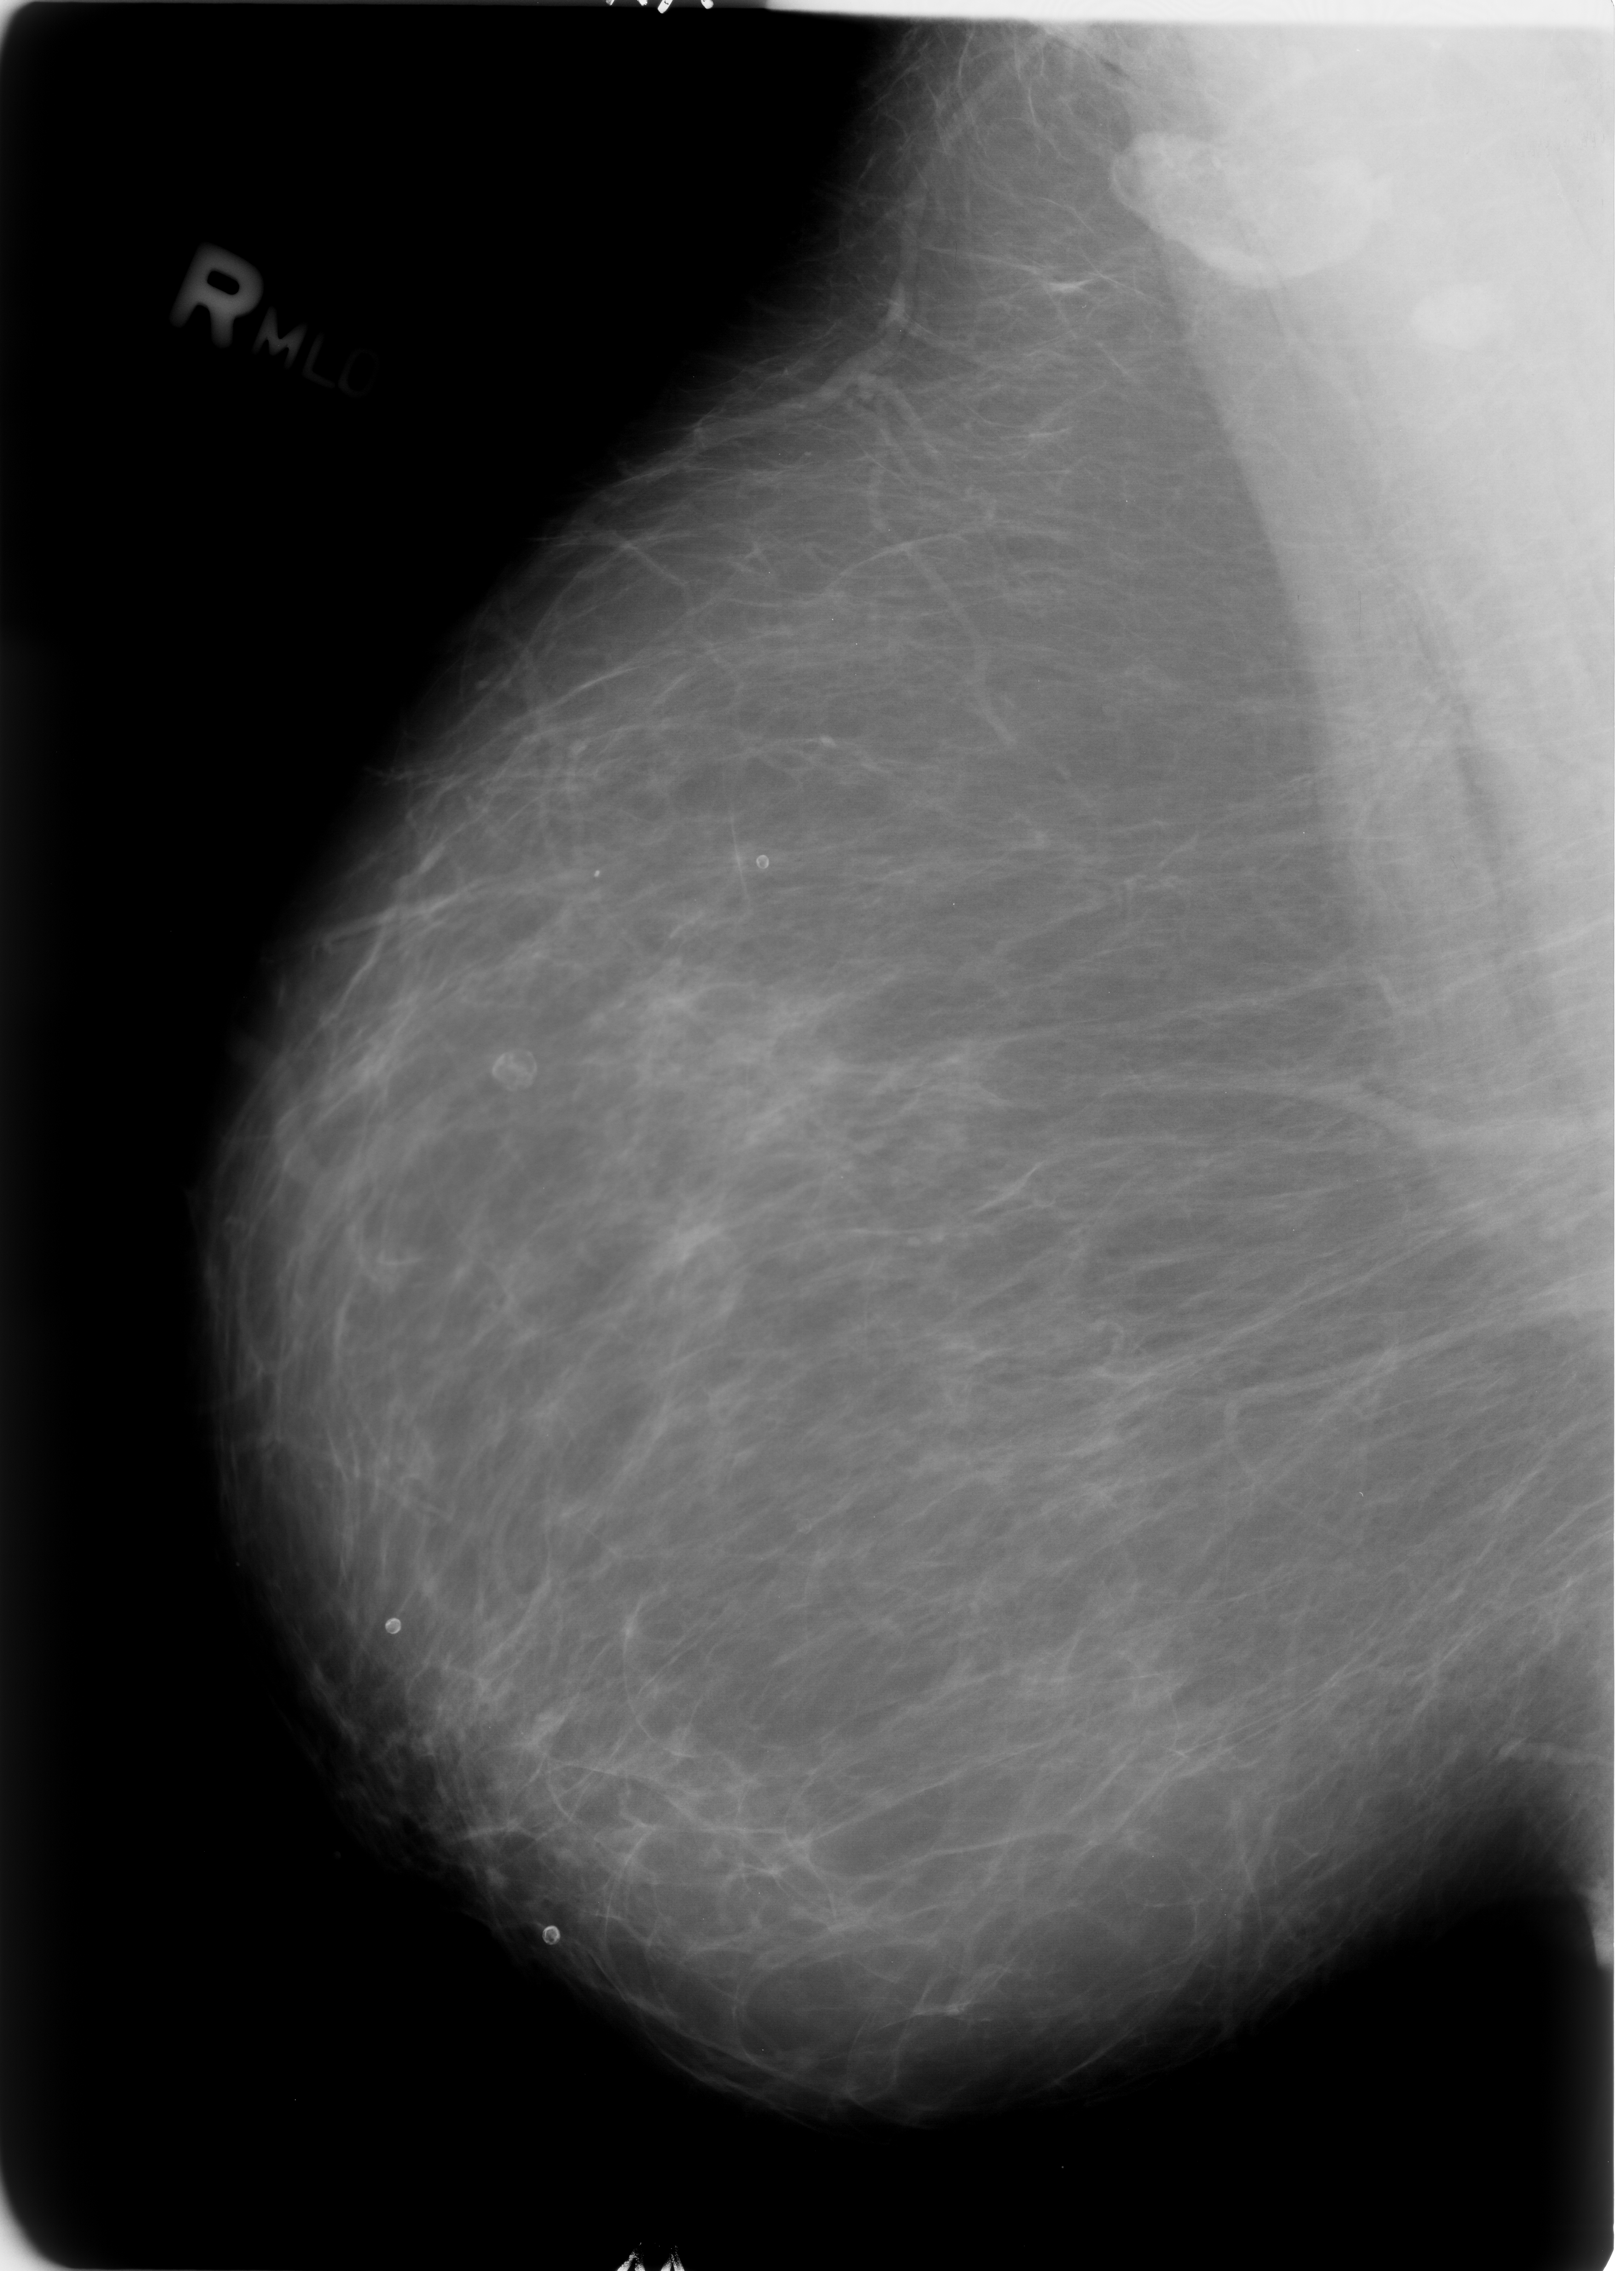
Scanned film-screen mammogram. Right breast. Mediolateral oblique (MLO) view. Breast composition: almost entirely fatty (BI-RADS density category 1 of 4). 1624 × 2271 image matrix.
Expert-marked regions of interest on this film, with their recorded descriptors:
- Finding 1 of 2: calcifications, morphology eggshell; BI-RADS assessment category 2; subtlety rating 5 on a 1 (subtle) to 5 (obvious) scale; benign; no additional work-up was recommended (outcome (as recorded, no biopsy): benign without callback): bounding box <479,1047,543,1095> (left, top, right, bottom; pixels)
- Finding 2 of 2: calcifications, morphology eggshell; BI-RADS assessment category 2; outcome (as recorded, no biopsy): benign without callback (not worked up further): <737,842,780,887>